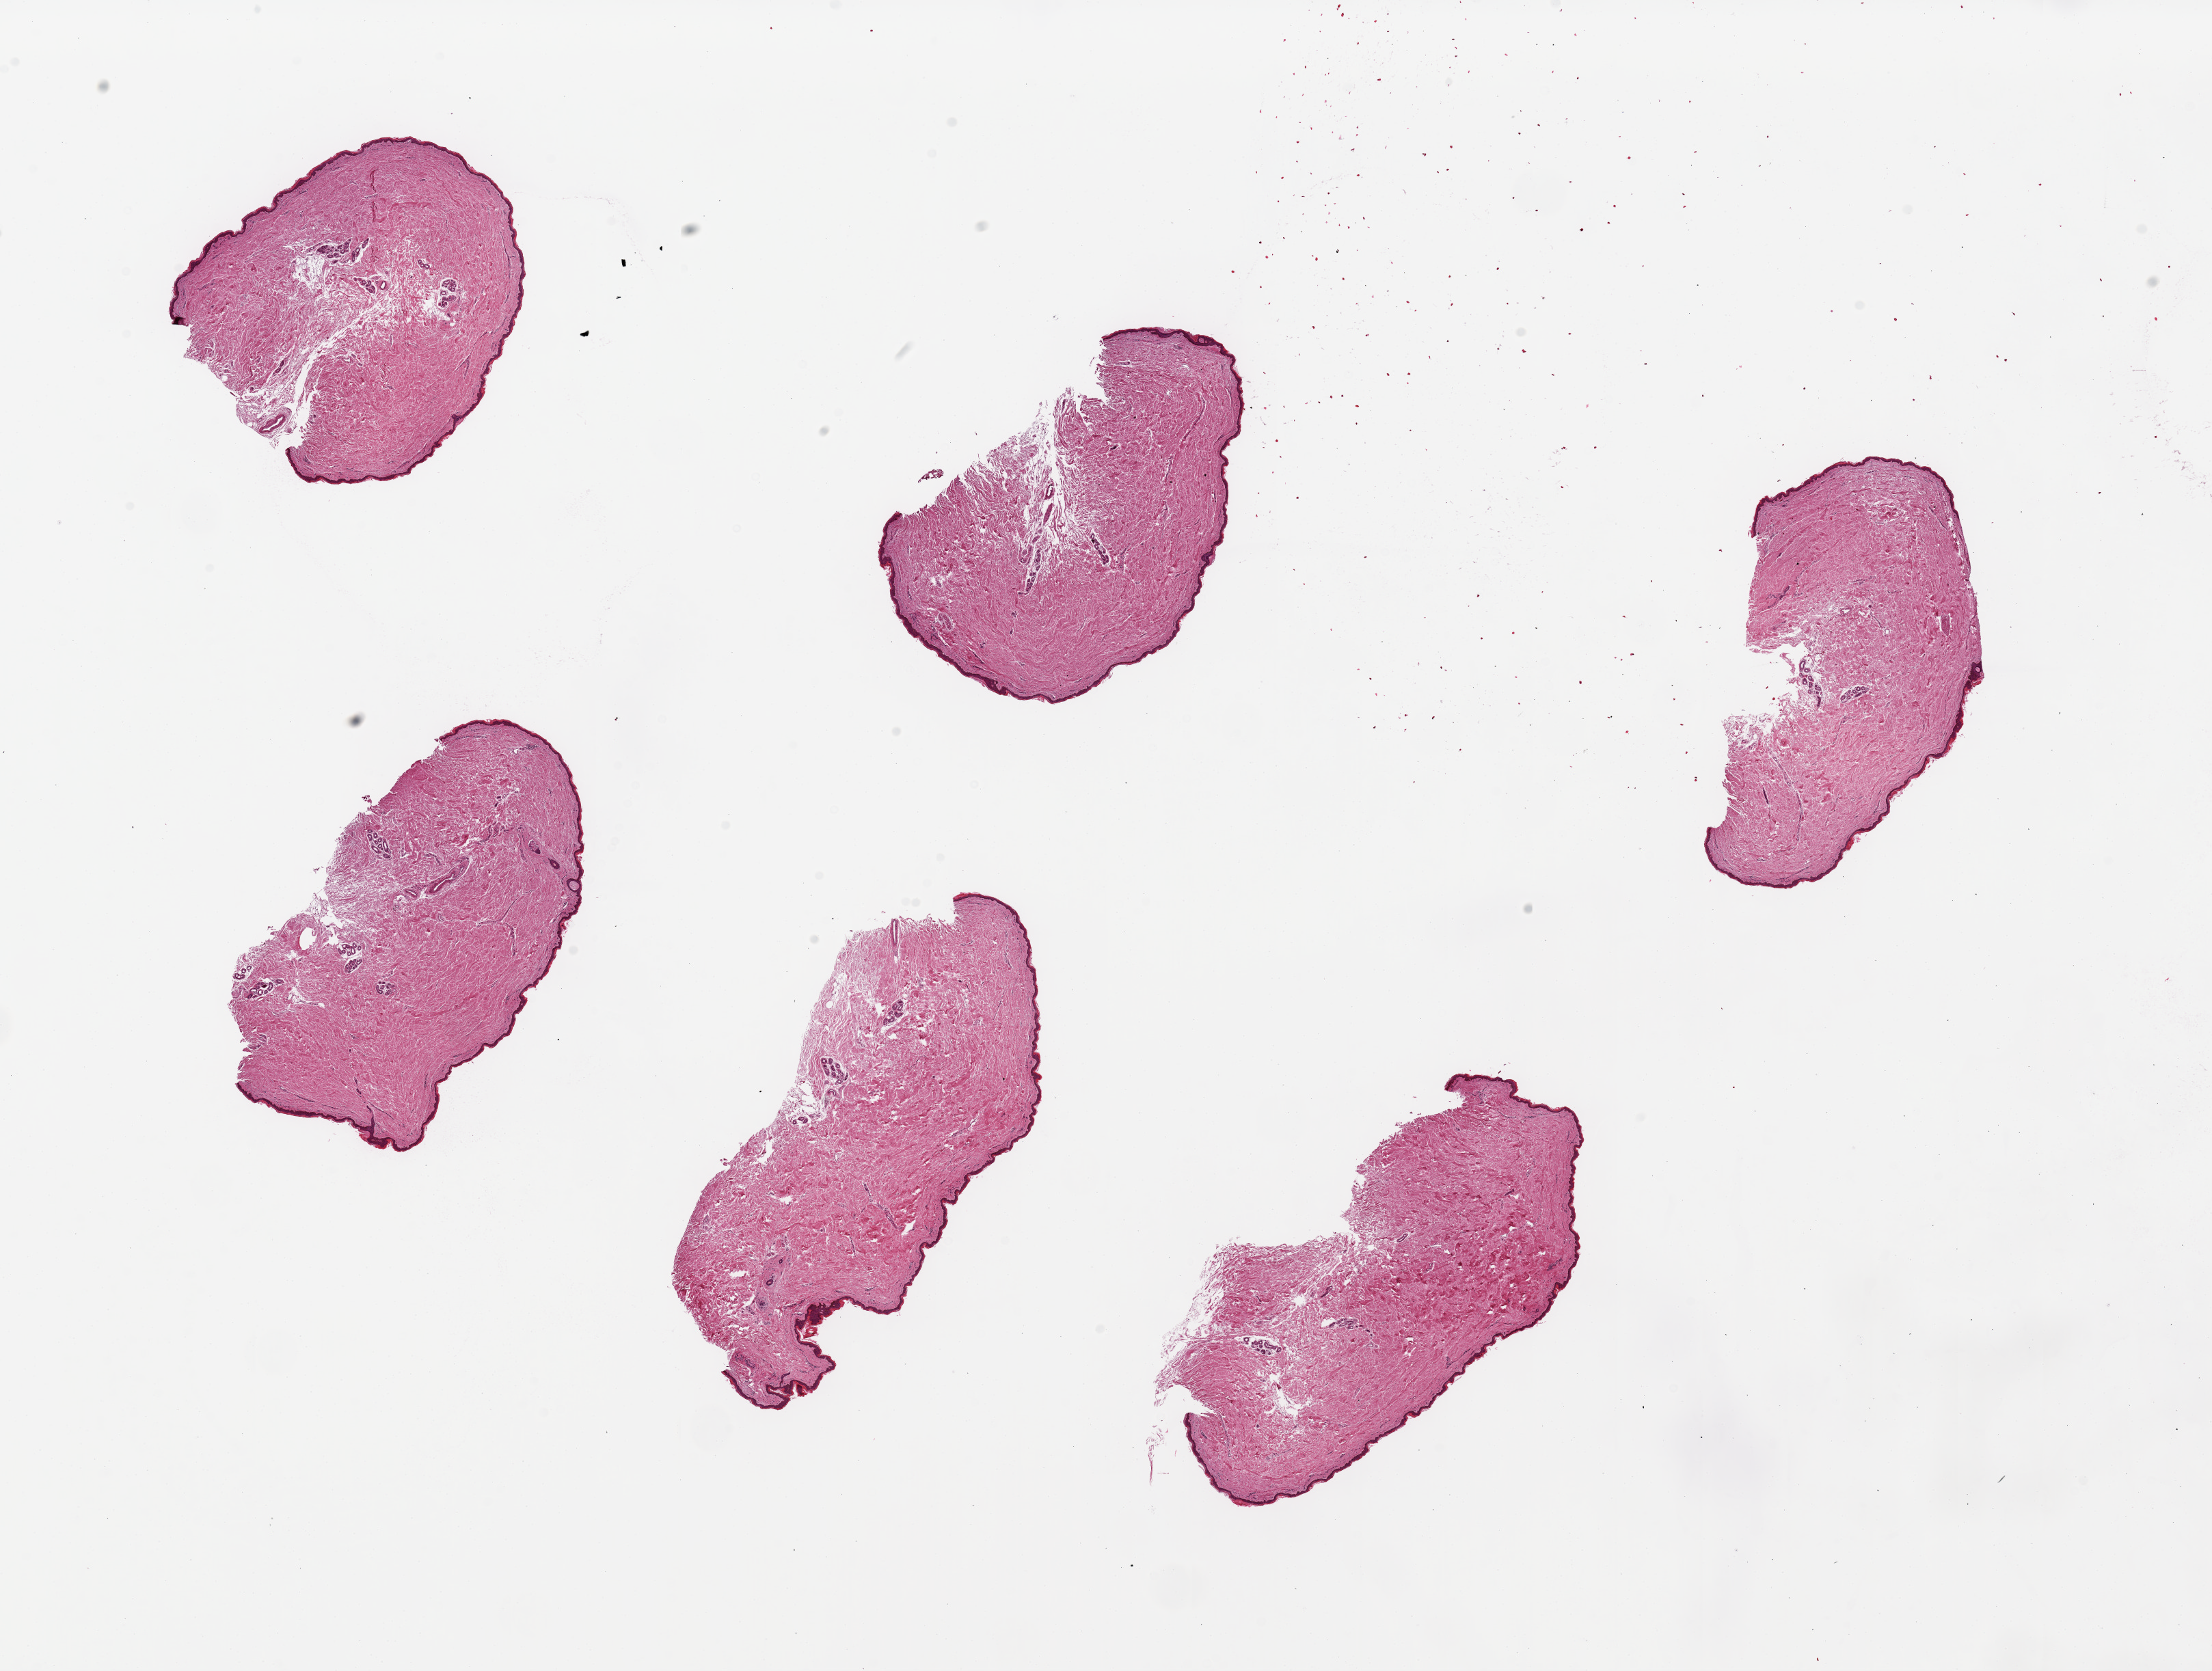
Digitized H&E-stained section — whole scanned area (about 25.6 x 19.3 mm) shown as a low-resolution overview; PAXgene-fixed paraffin-embedded (PFPE) section; sampled site (target tissue): skin of suprapubic region; donor tissue sample. Female donor.
• reviewer comment on this tissue sample: 6 pieces, up to 6x3mm; well trimmed